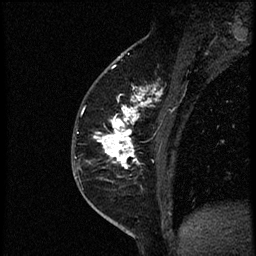
Breast MRI (dynamic contrast-enhanced), one sagittal slice. Position 26 of 56 along the scan axis. Dynamic contrast-enhanced study with each time point stored as its own series, time point 2 of 4 at this slice position (early post-contrast, ordered by acquisition time). 1.5 T. TE 4.2 ms, TR 18.9 ms. 256 × 256 image matrix, field of view 200 × 200 mm. Female patient. From the clinical record (not read from this slice): setting: breast cancer imaged before/during neoadjuvant chemotherapy; receptor status: HER2-positive.
Structures marked on this image (semi-automatically segmented with operator editing):
- analysis volume of interest (the breast-tissue region the enhancement analysis was run in; not a lesion): box from (x=89, y=86) to (x=174, y=189) px
- tumour enhancement mask (voxels above the 100 % enhancement threshold inside the analysis volume of interest): (x=95, y=89)–(x=152, y=177)